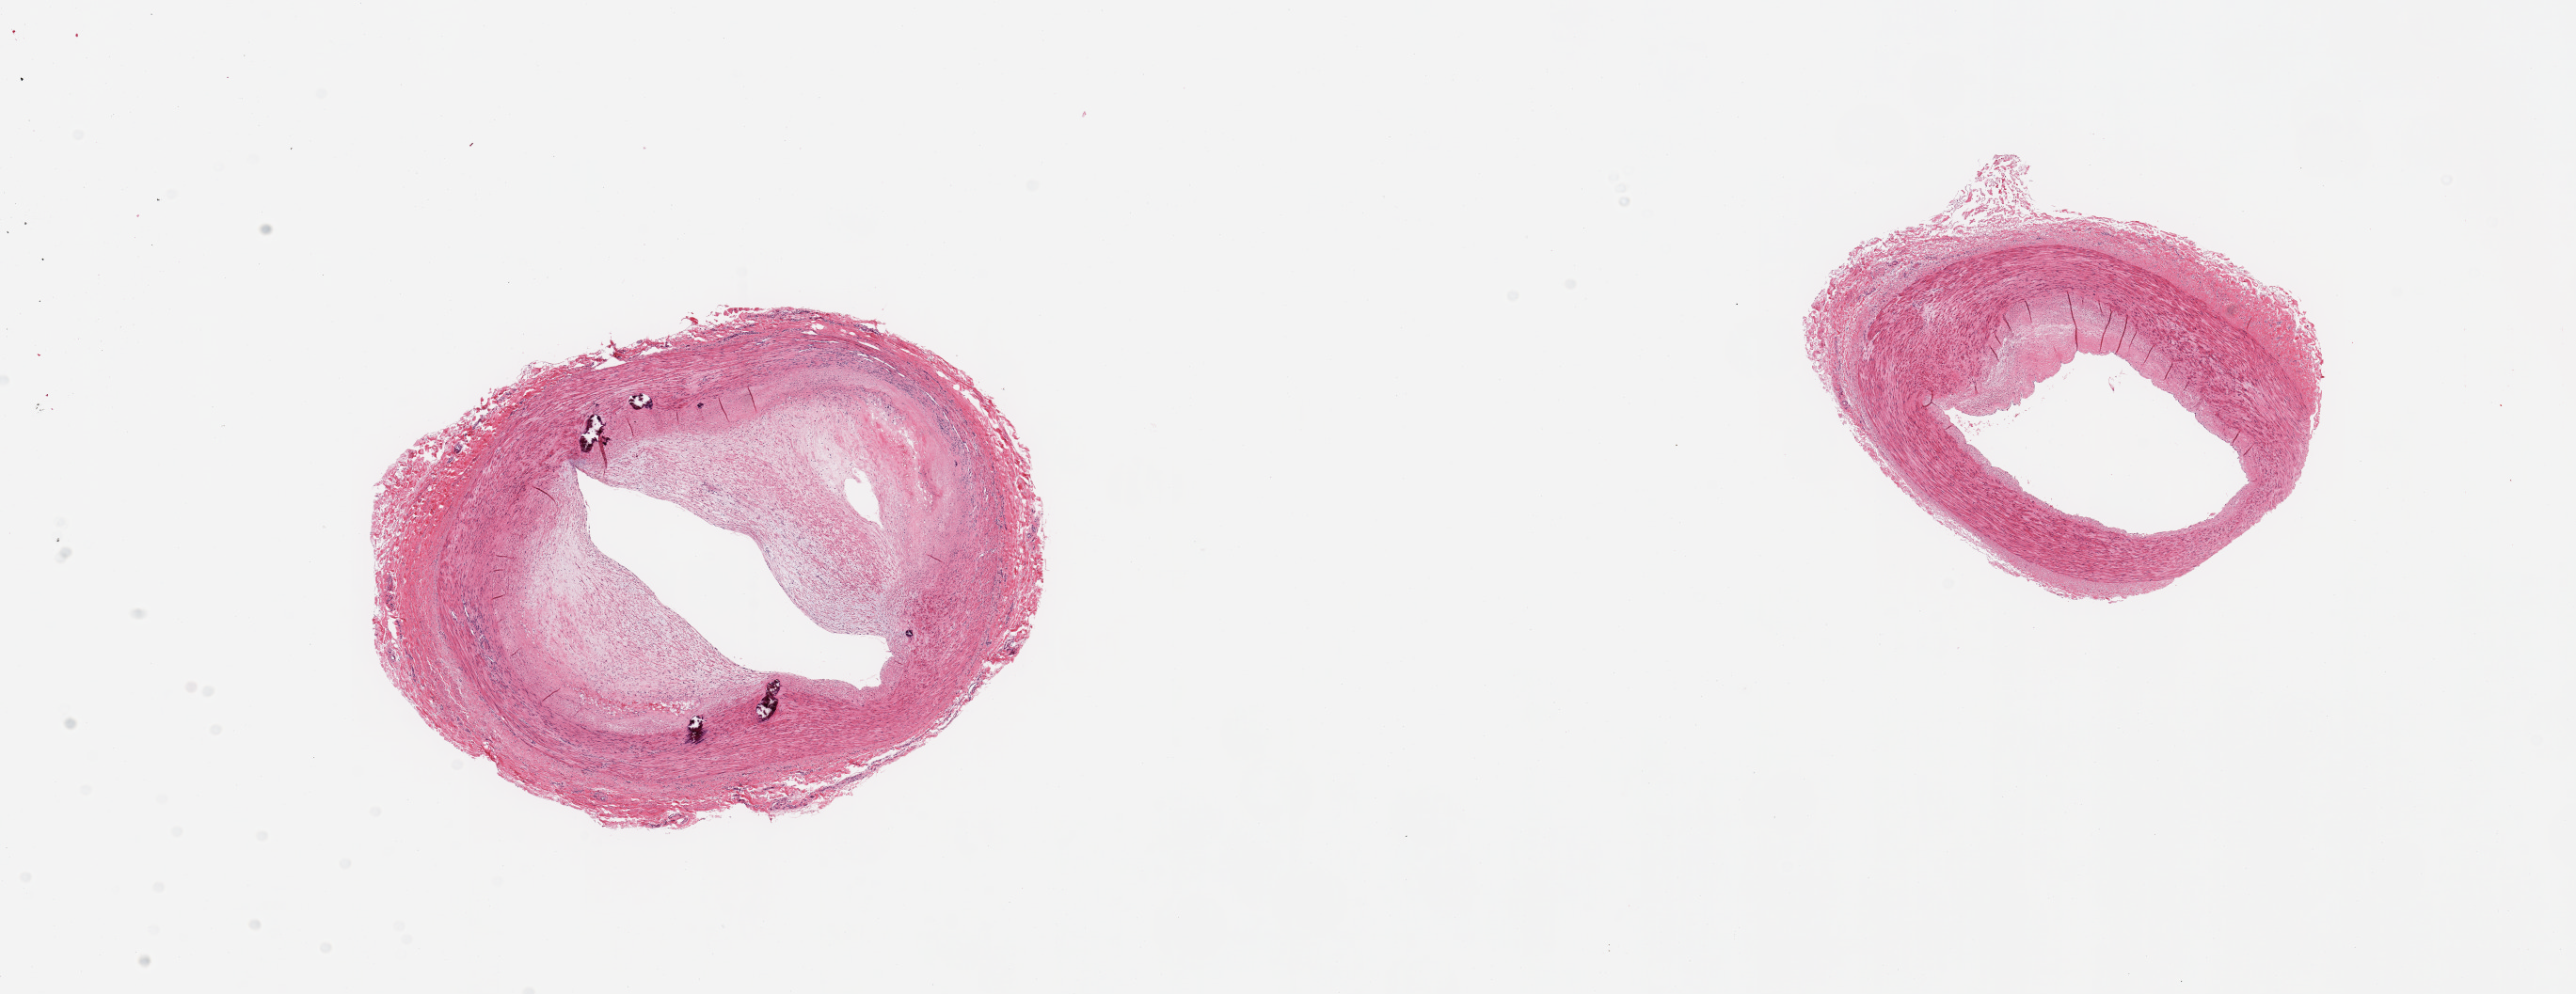
Digitized hematoxylin and eosin (H&E)-stained section — whole scanned area (about 21.7 x 8.4 mm) shown as a low-resolution overview, PAXgene-fixed paraffin-embedded (PFPE) section, sampled site (target tissue): tibial artery, tissue donor sample. Male donor.
- pathologist's review note for this sample: 2 pieces; atherosclerosis, focal medial calcification